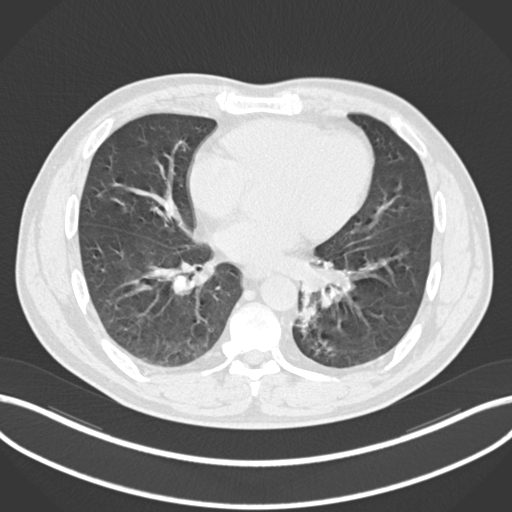
Chest CT, one axial slice. Slice 91 of 223 in the series (ordered by position). 120 kVp. Lung window (W 1500 / L -600 HU). 1 mm slice thickness. 512 × 512 image matrix, field of view 400 × 400 mm. Male patient, age 50 years. Case-level facts recorded for this patient, not image findings: clinical TNM (as recorded): T2a N3 M0.
Structures marked on this image (bounding box drawn by a radiologist):
- lung tumour (recorded histology: squamous cell carcinoma): bounding box (x1, y1, x2, y2) in pixels: (294, 289, 322, 339)